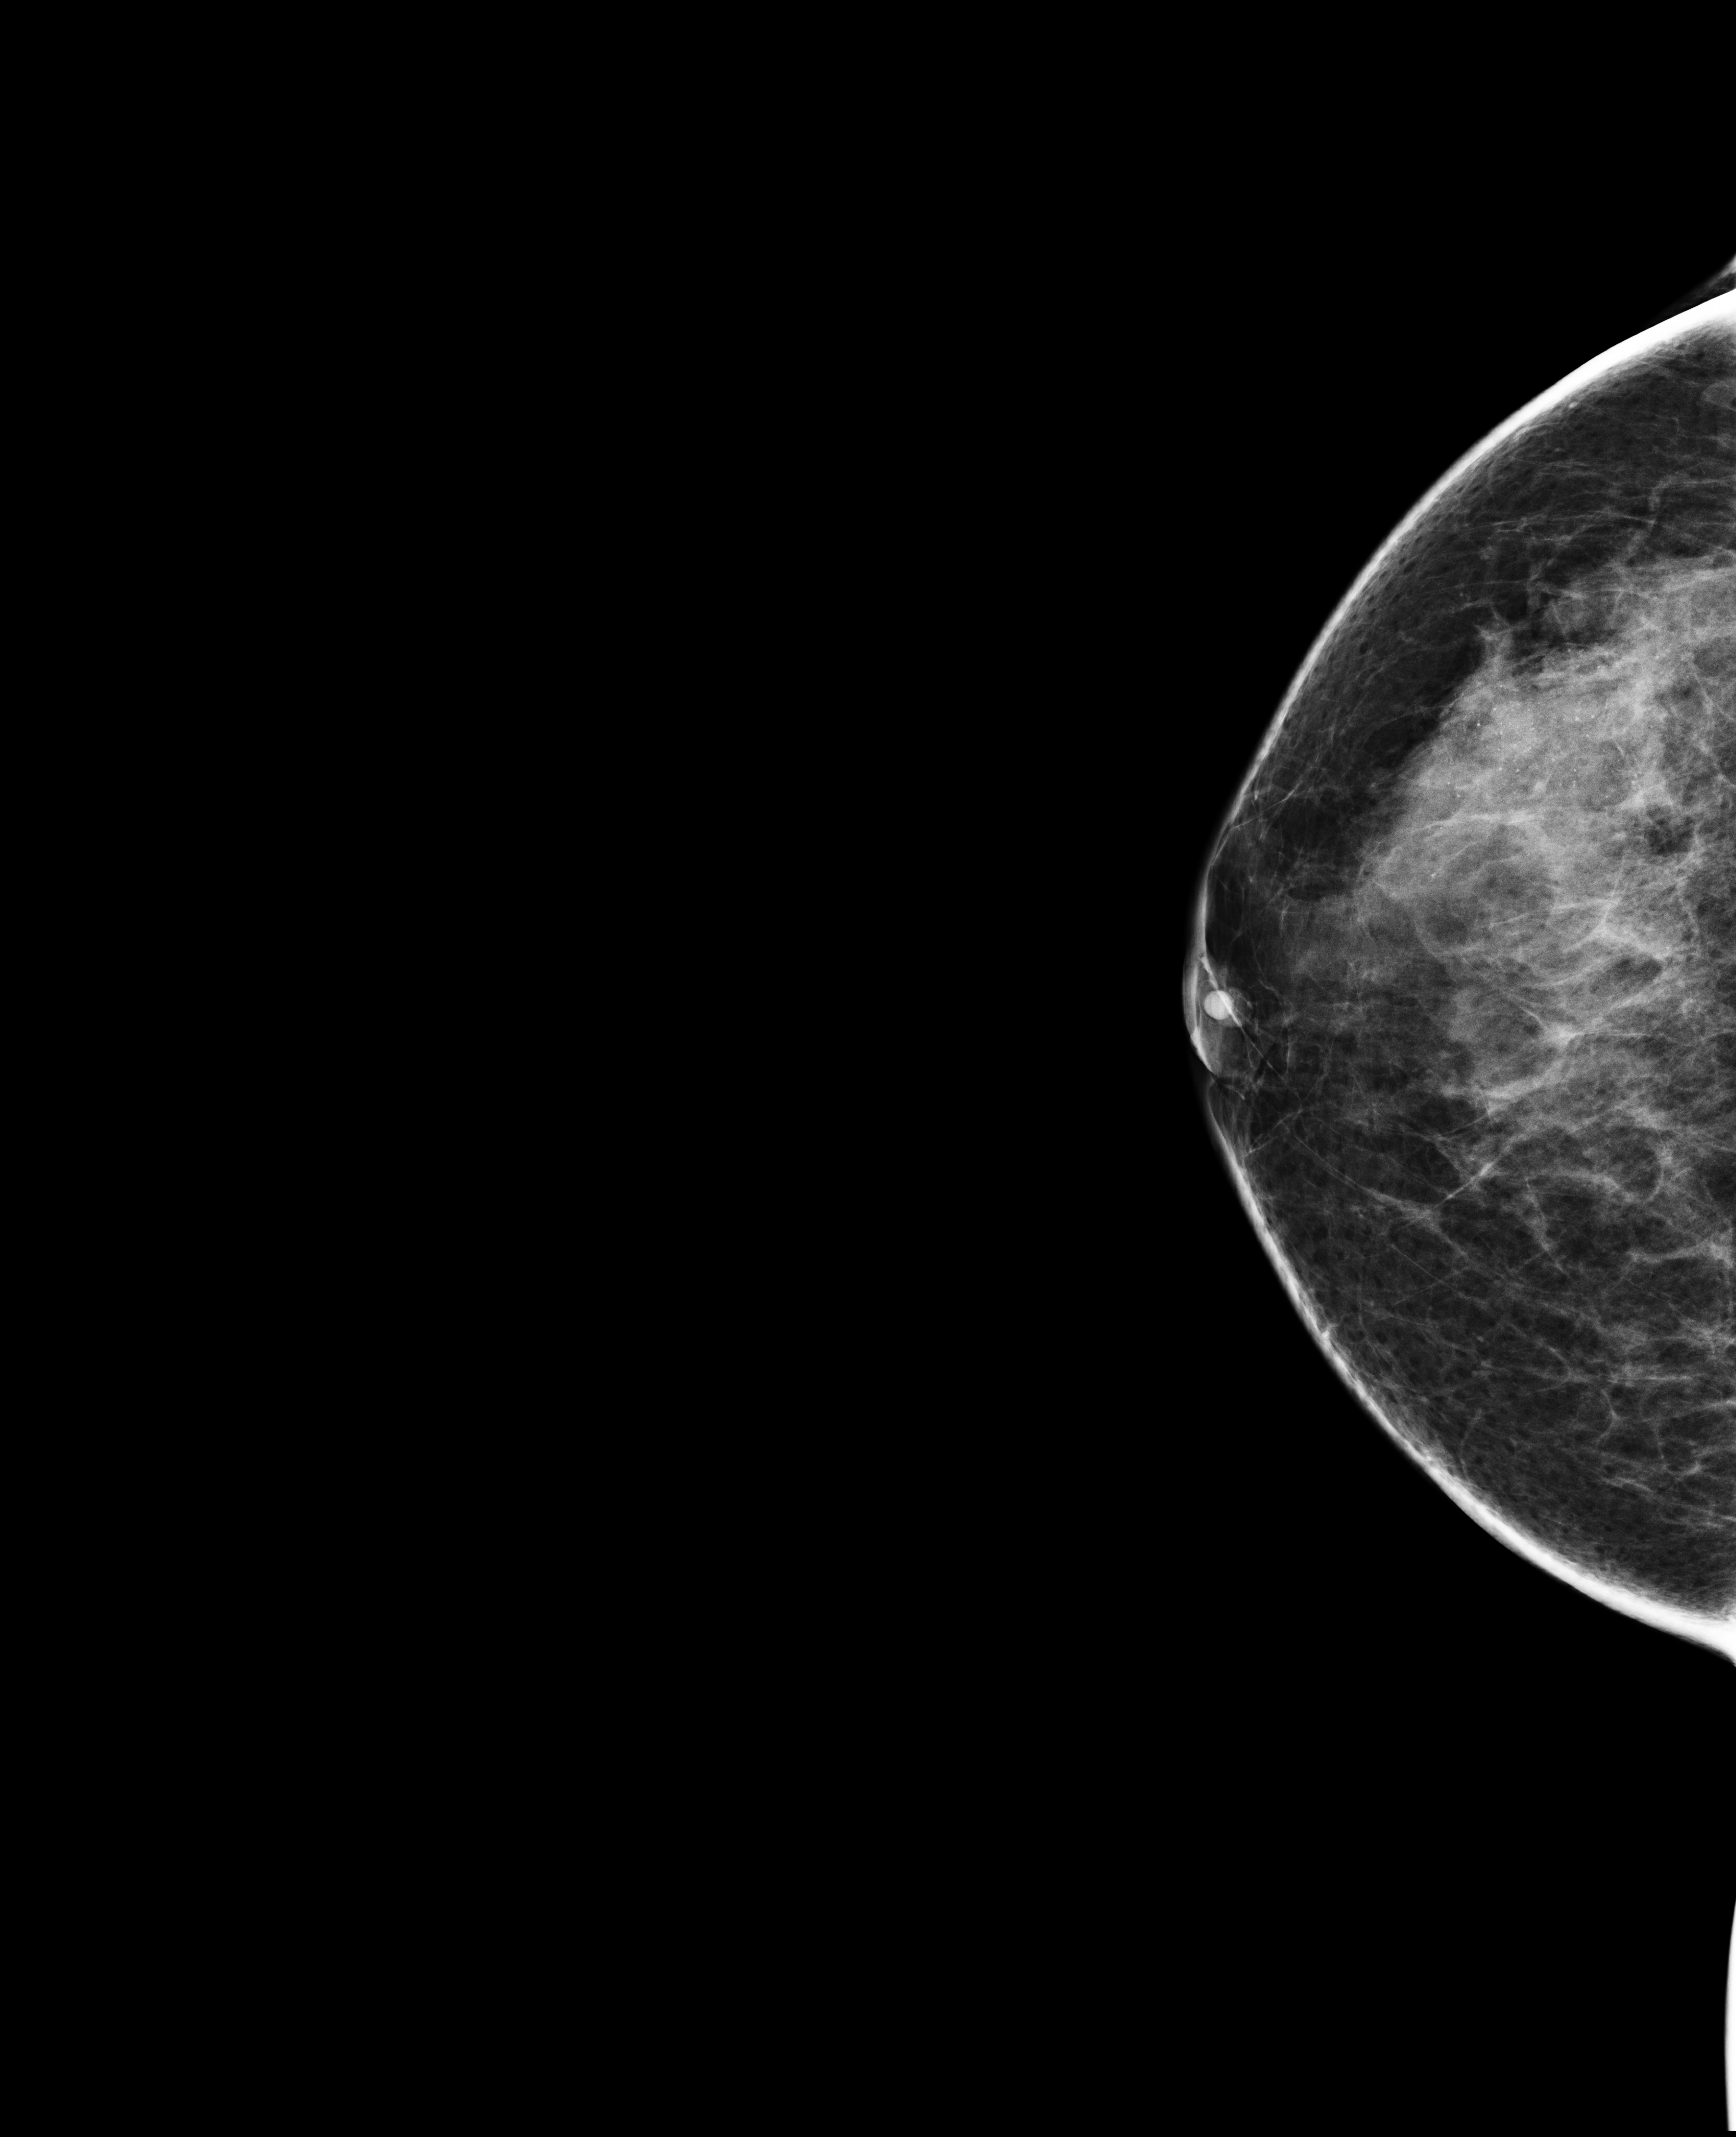
Digital mammogram (FFDM); right breast; cranio-caudal projection; screening examination; system: Selenia Dimensions. Patient: female, 48 years.
- BI-RADS breast density category at the screening exam (both breasts, scale 1–4): 3
- final BI-RADS assessment for this screening round (tomosynthesis exam, both breasts): category 4
- recall: recalled for additional imaging after this screen